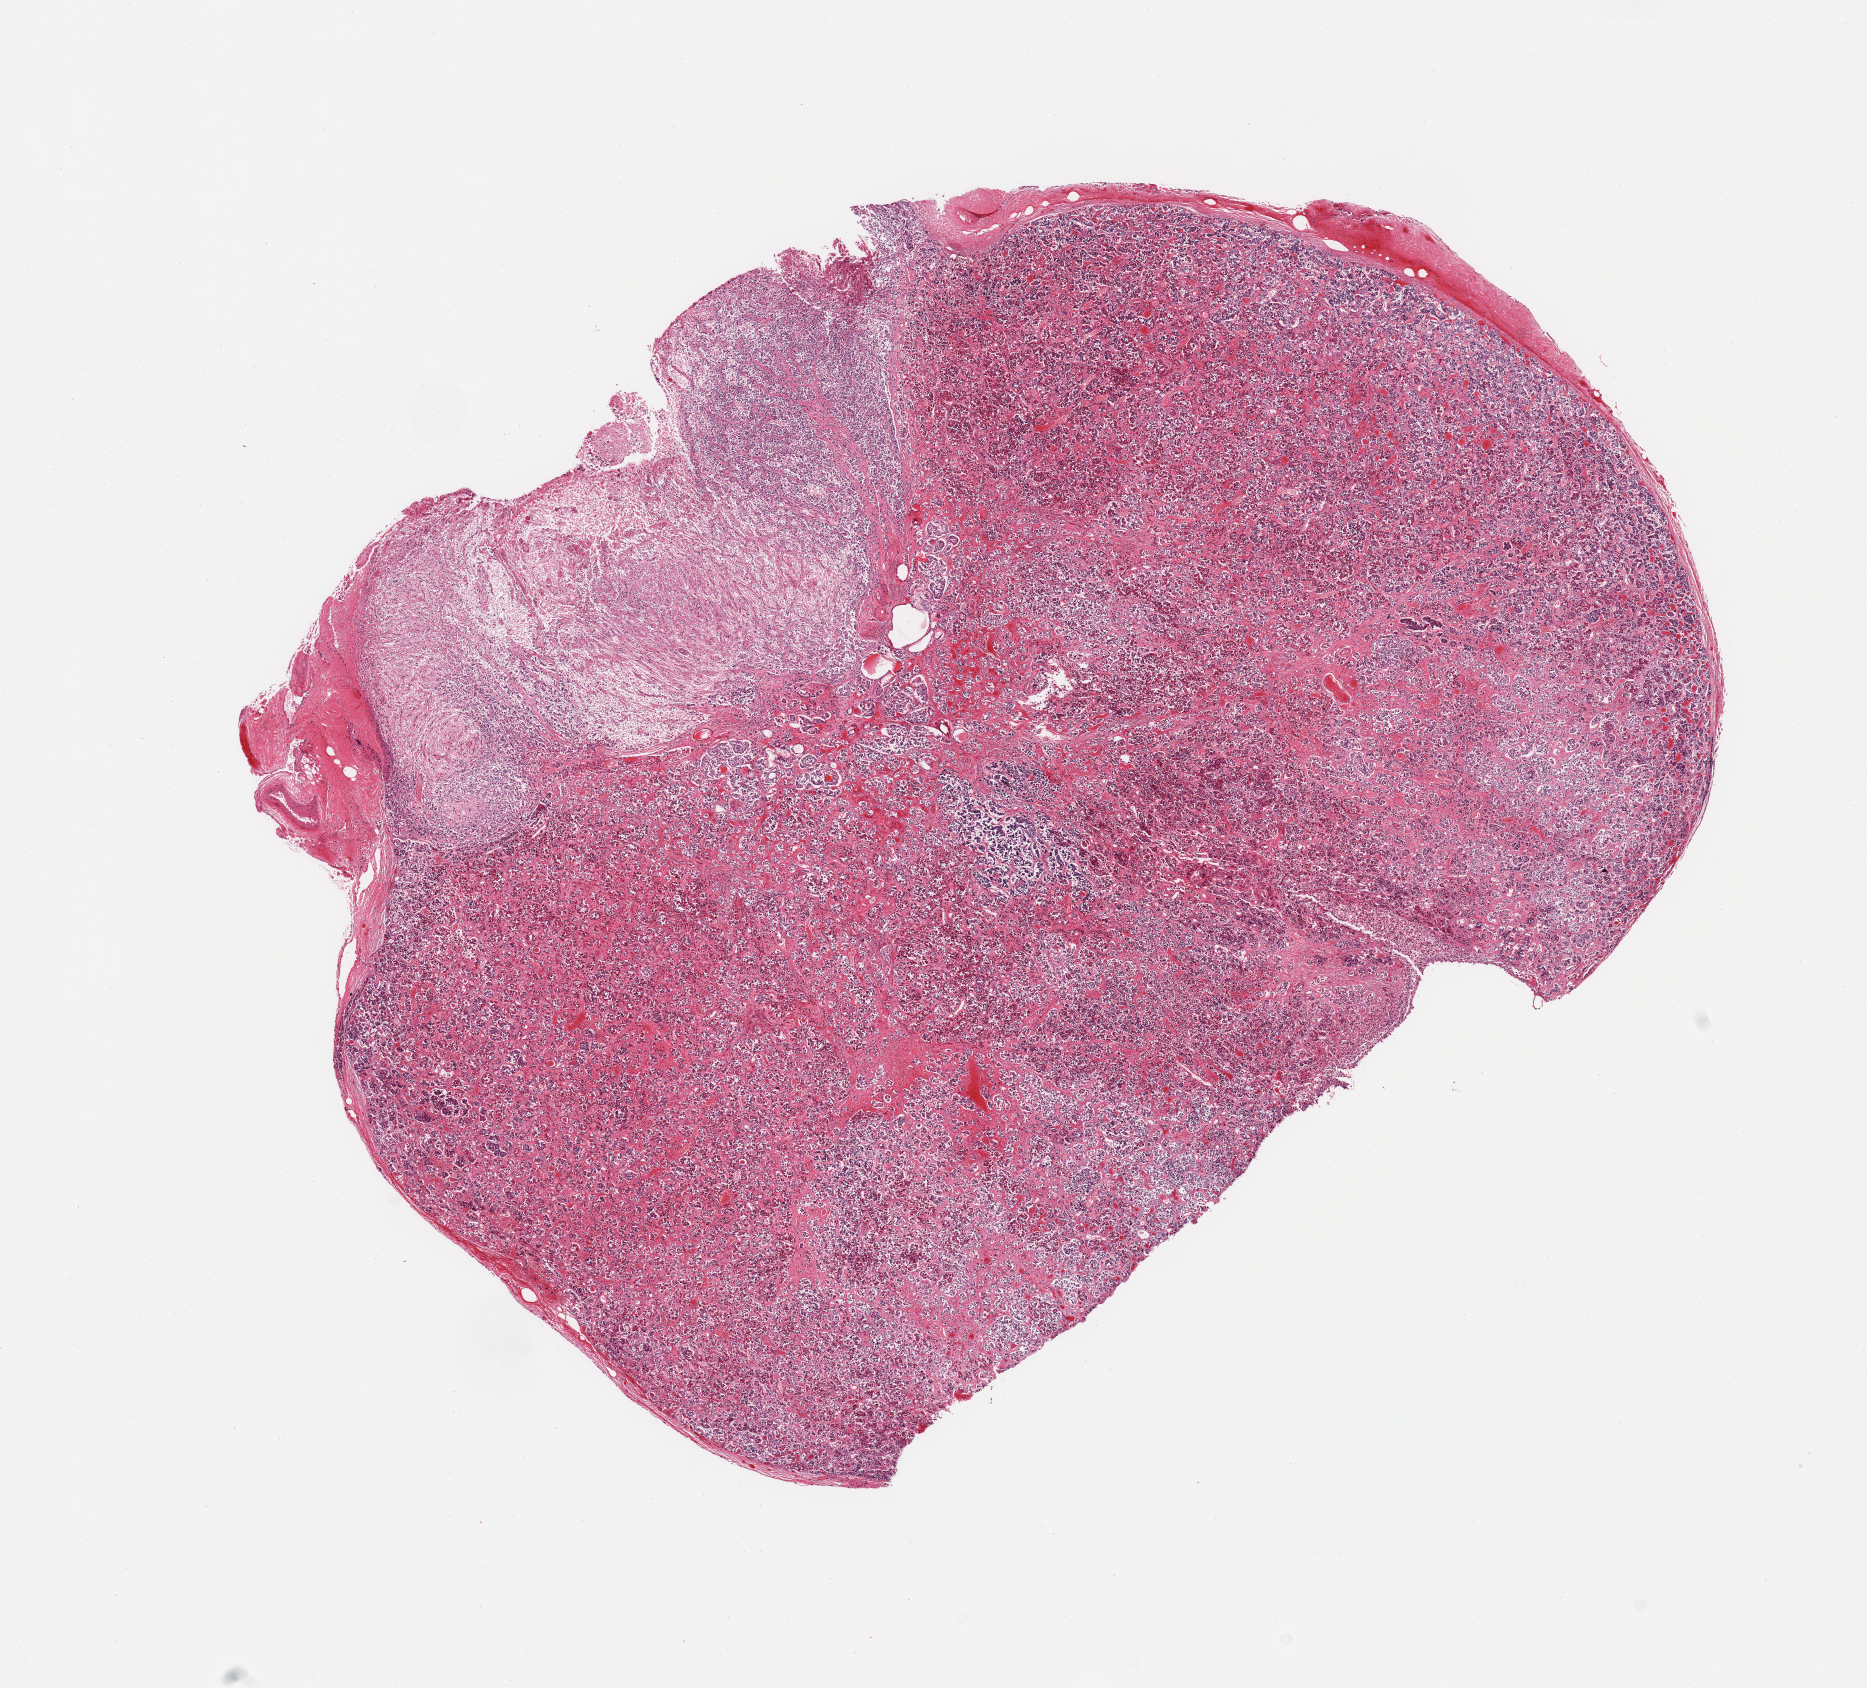
Whole-slide image, hematoxylin and eosin (H&E) stain — low-resolution overview of the scanned area, about 14.8 x 13.4 mm (from a 20x scan); PAXgene-fixed paraffin-embedded (PFPE) section; sampled site (target tissue): pituitary; donor tissue sample. Donor sex: male.
Pathologist's review note for this sample: 1 piece, mainly adenohypophysis; ~3x2.5mm focus of neurohypophysis.